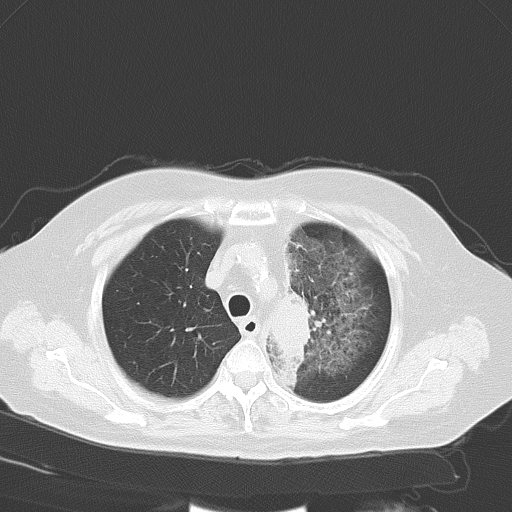
Chest CT, one axial slice. Reconstruction kernel B70f. 120 kVp. Lung window (W 1500 / L -600 HU). 5 mm slice thickness. 512 × 512 image matrix, field of view 353 × 353 mm. Patient: female, 65 years. From the clinical record (not read from this slice): clinical TNM (as recorded): T2b N1 M0.
Outlined on this slice (rectangle marked by the reading radiologist):
- lung tumour (recorded histology: adenocarcinoma): bounding box (x1, y1, x2, y2) in pixels: (272, 290, 316, 374)